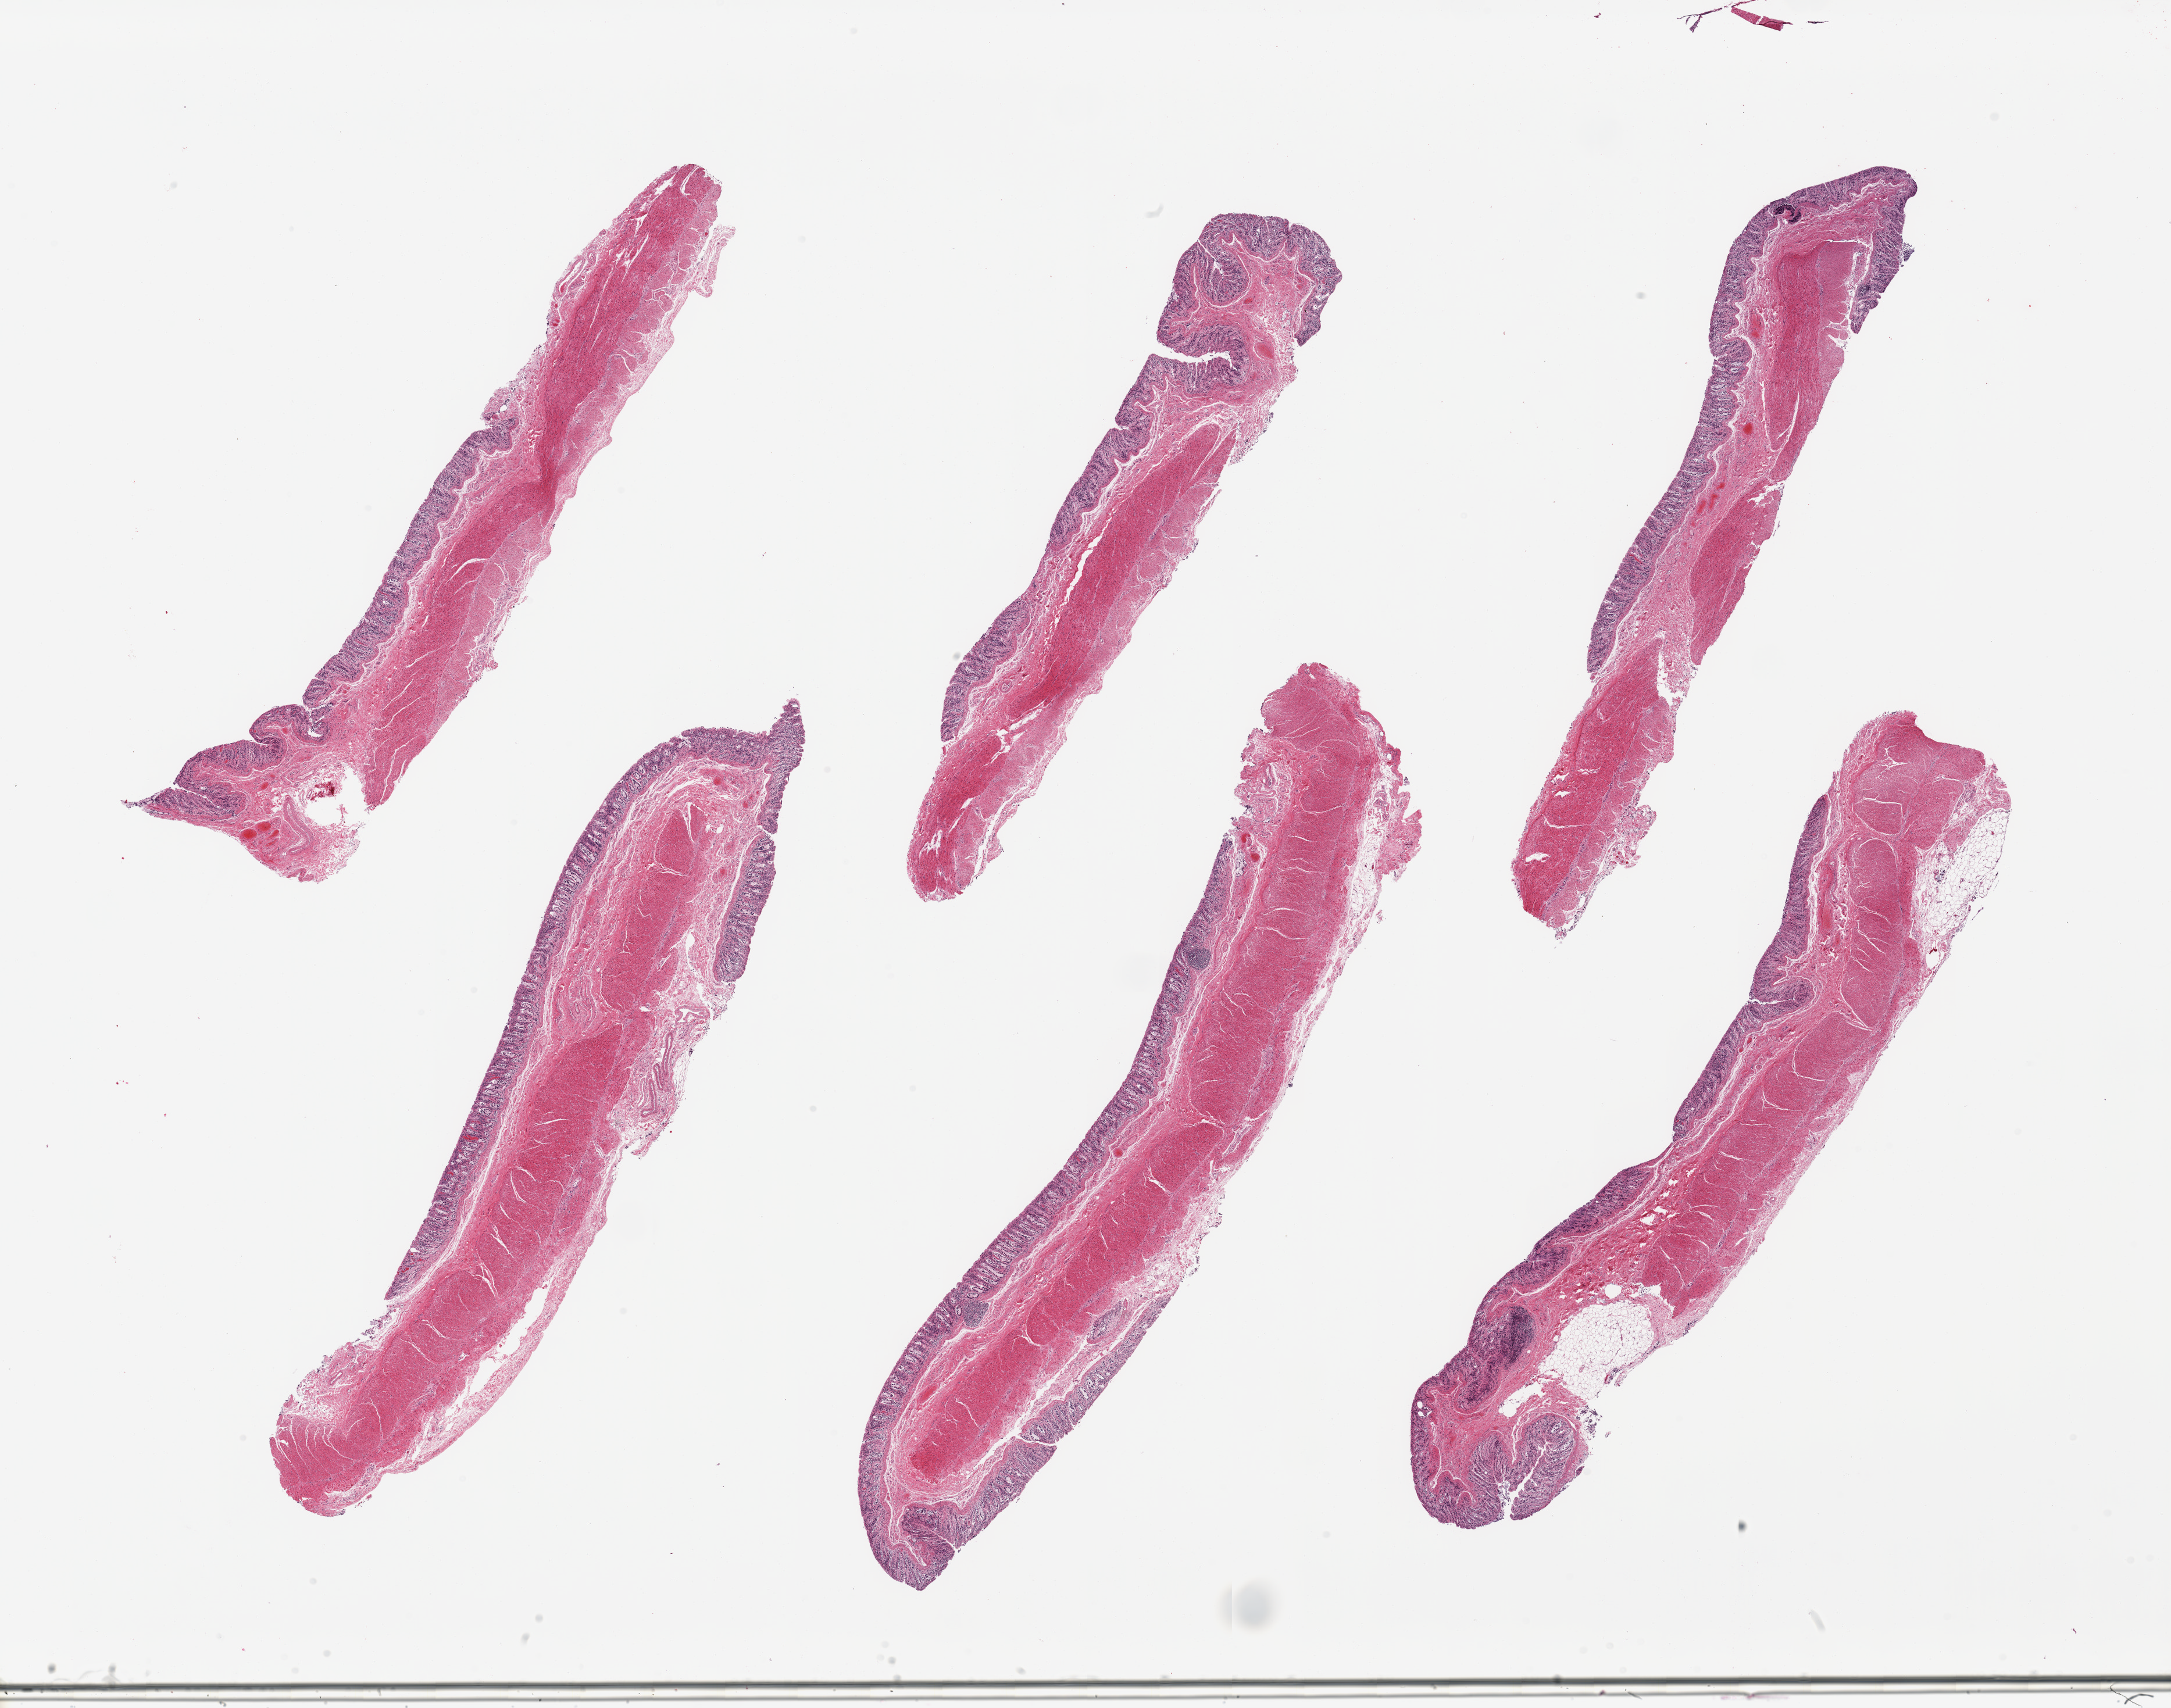
Whole-slide image, hematoxylin and eosin (H&E) stain, a low-resolution overview of the entire scanned area, about 29.5 x 23.2 mm (slide scanned at 20x); PAXgene-fixed paraffin-embedded (PFPE) section; section of transverse colon (target tissue); tissue donor sample. Donor: male.
Reviewer comment on this tissue sample: 6 pieces; moderately autolyzed mucosa and preserved muscularis.